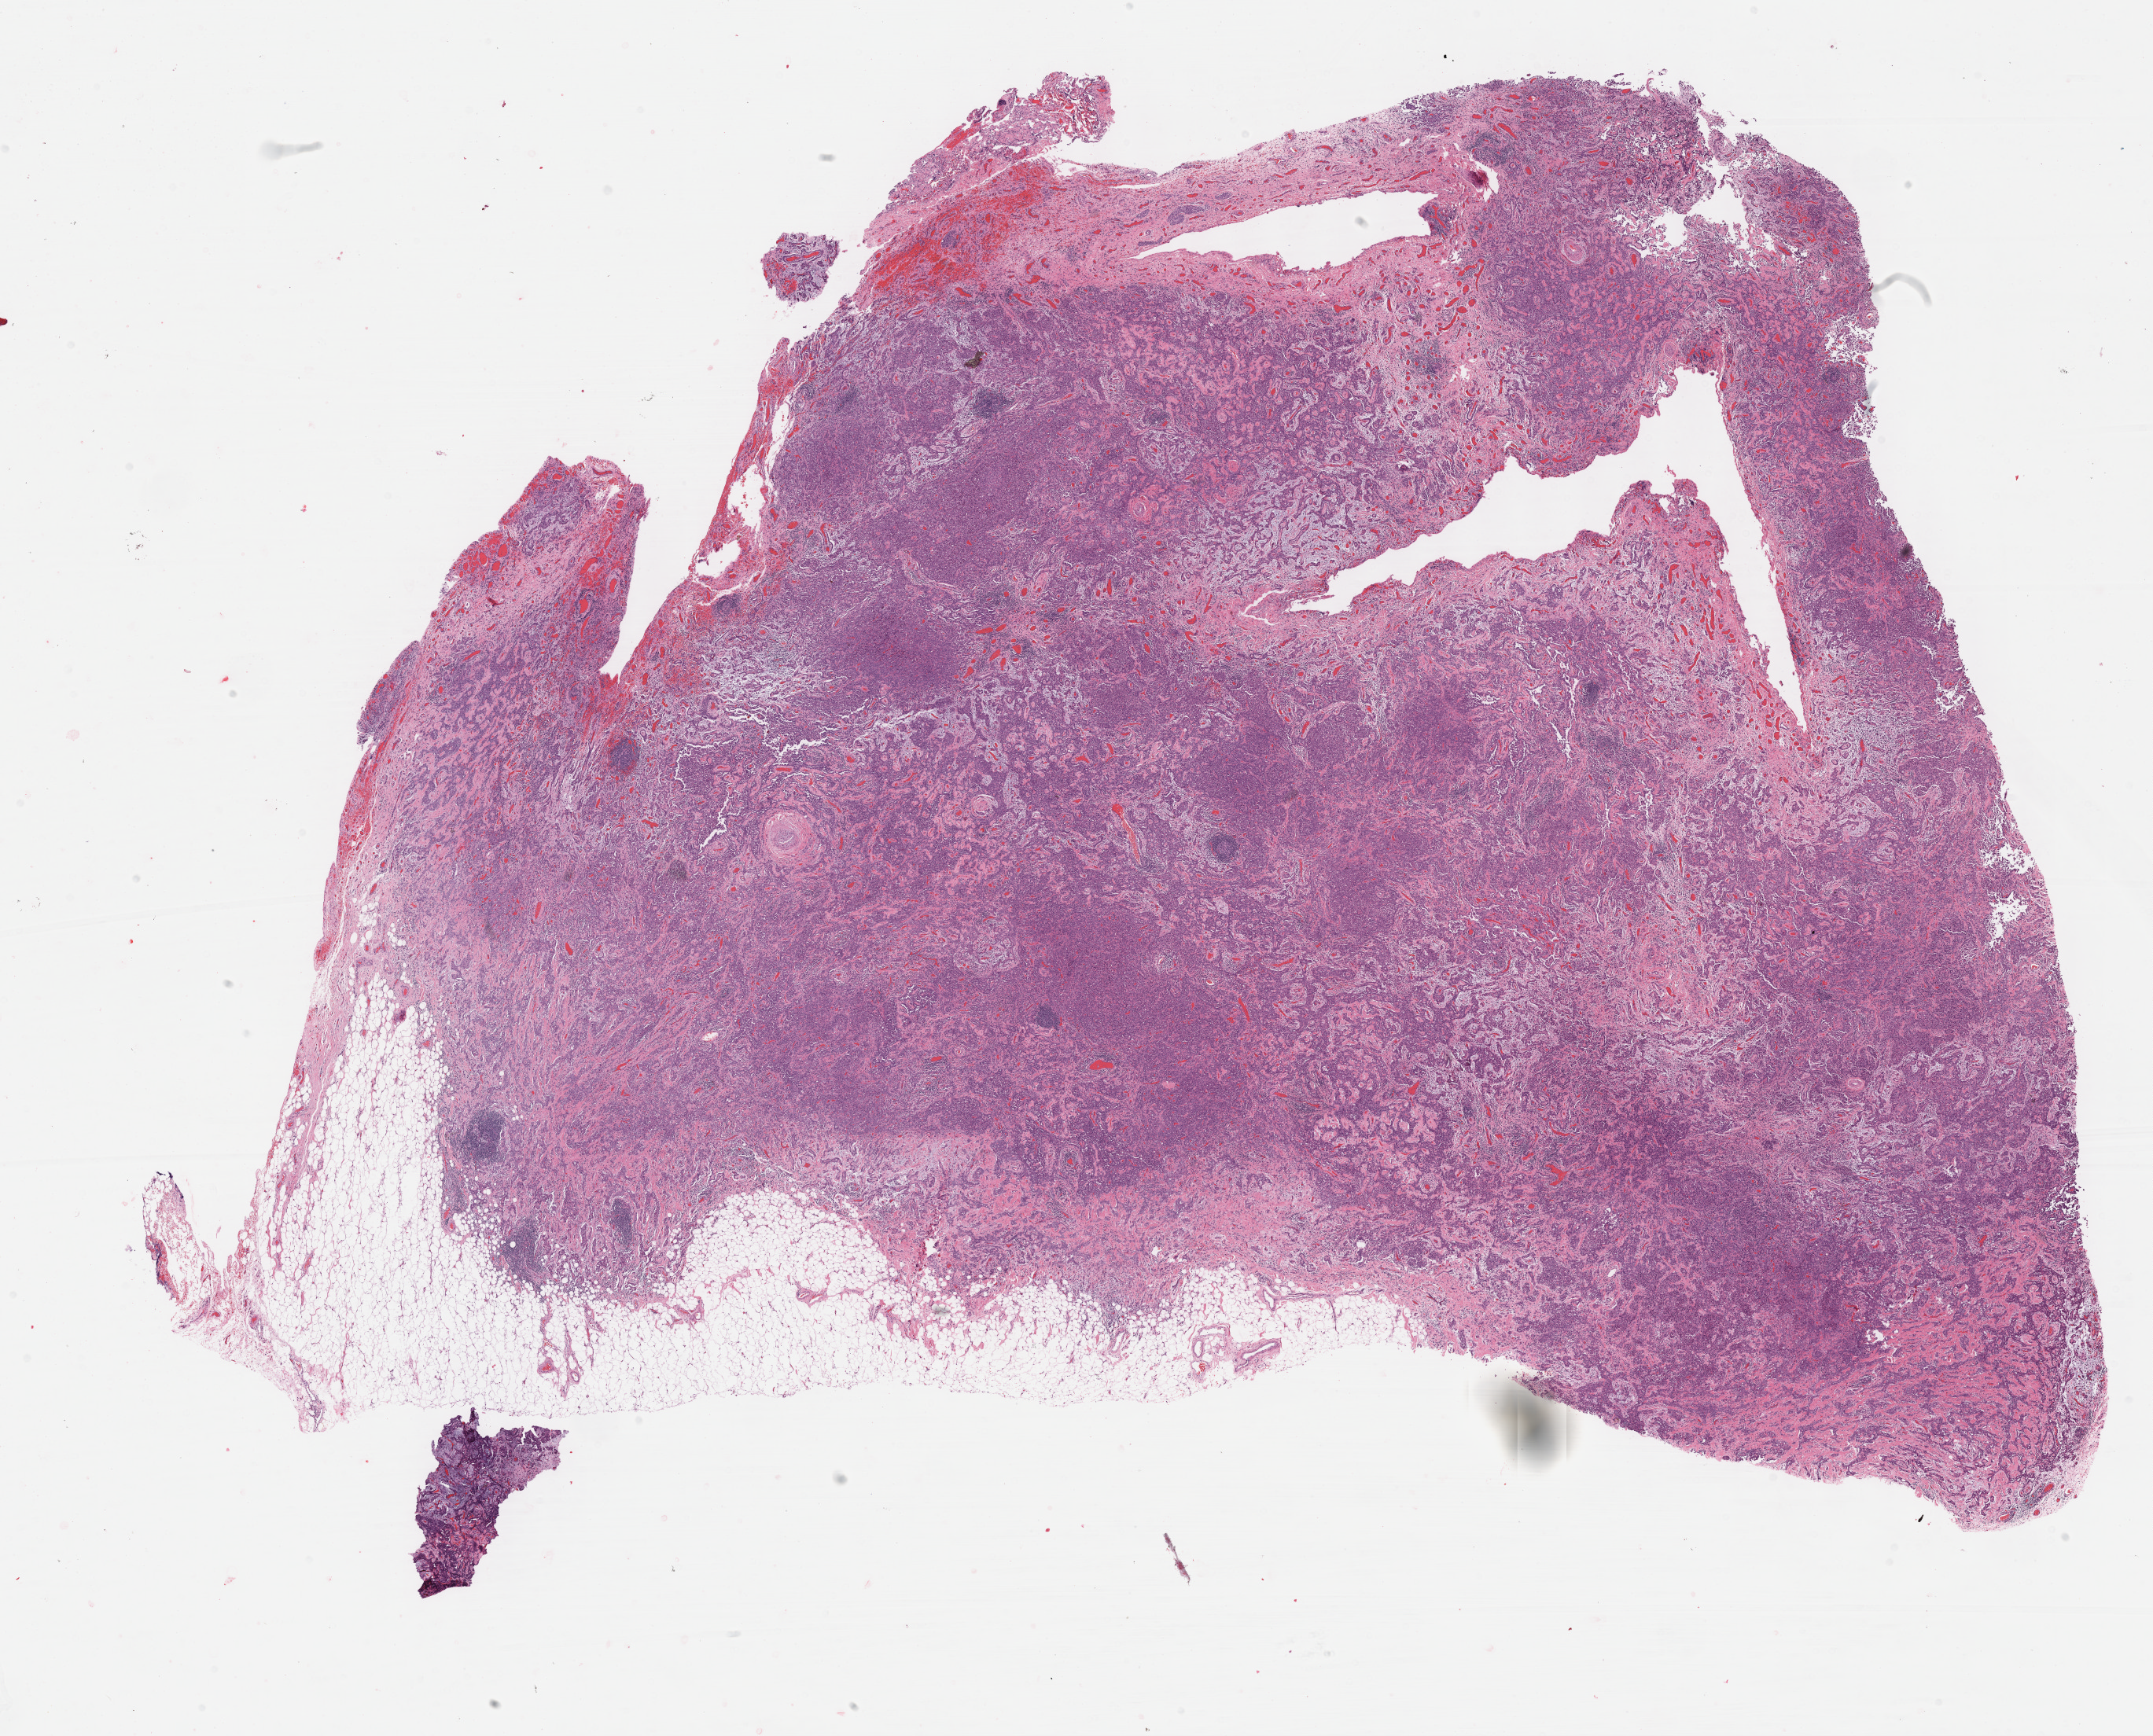
H&E-stained whole-slide image — a low-resolution overview of the entire scanned area, about 22.1 x 17.9 mm (from a 40x scan), formalin-fixed paraffin-embedded (FFPE) diagnostic section, sample: primary tumour, mesothelium. Patient: female, age at initial diagnosis 48 years.
Pathologic diagnosis: Epithelioid mesothelioma, malignant (pleura, NOS). TNM: T3 N1 MX. AJCC pathologic stage: III.